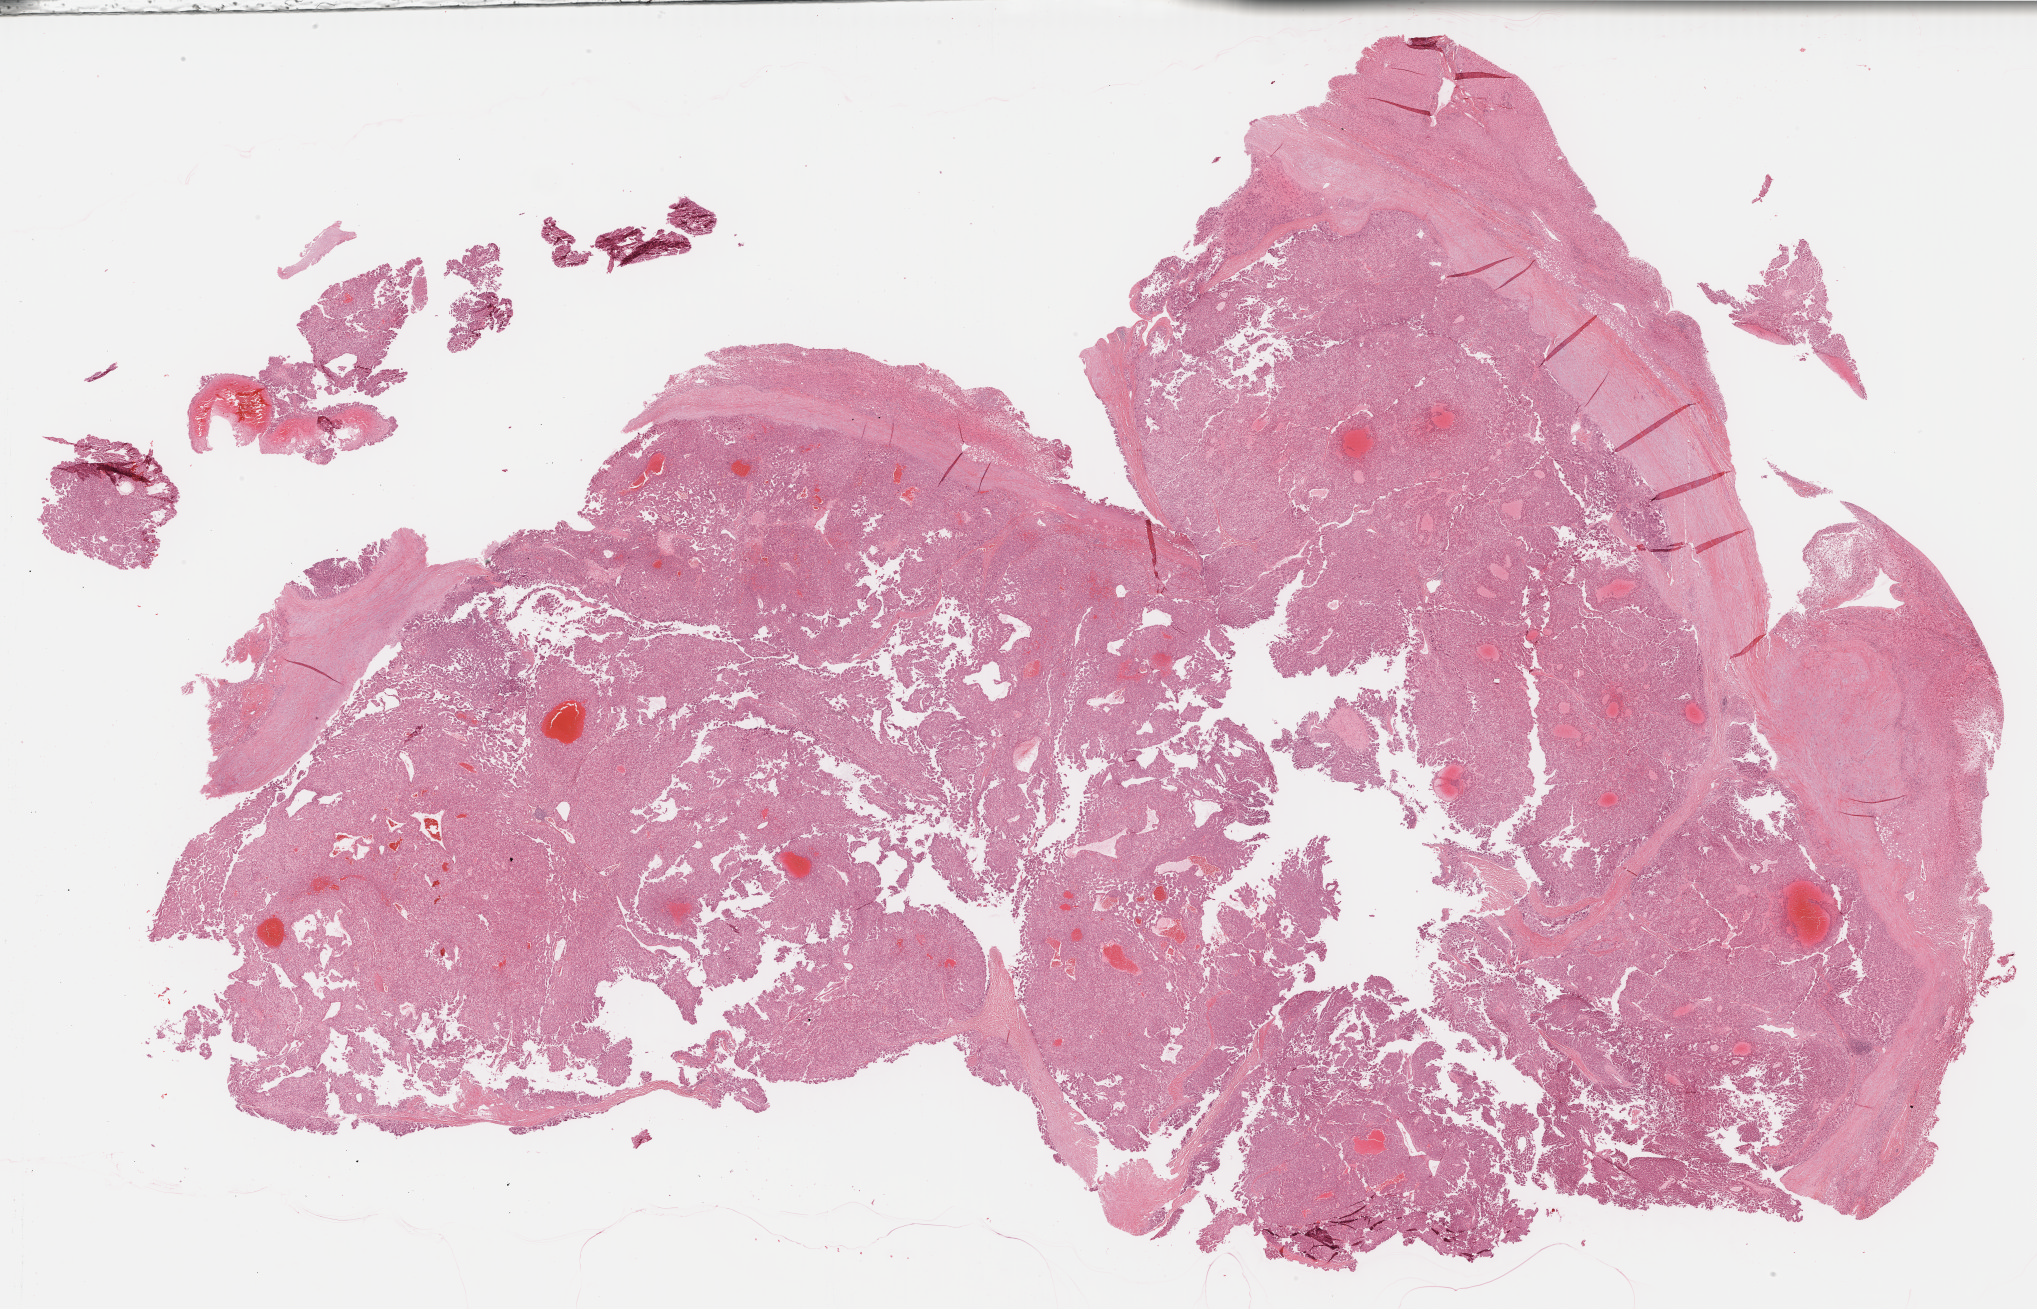
Digitized H&E tissue section (whole slide), whole scanned area (about 33.0 x 21.2 mm) shown as a low-resolution overview; formalin-fixed paraffin-embedded (FFPE) diagnostic section; sample: primary tumour, liver. Female patient; age at initial diagnosis 29 years. Histologic grade: G2 (moderately differentiated).
- TNM: T3 N0 M0
- AJCC pathologic stage: III (4th edition)
- histologic diagnosis: Hepatocellular carcinoma, NOS